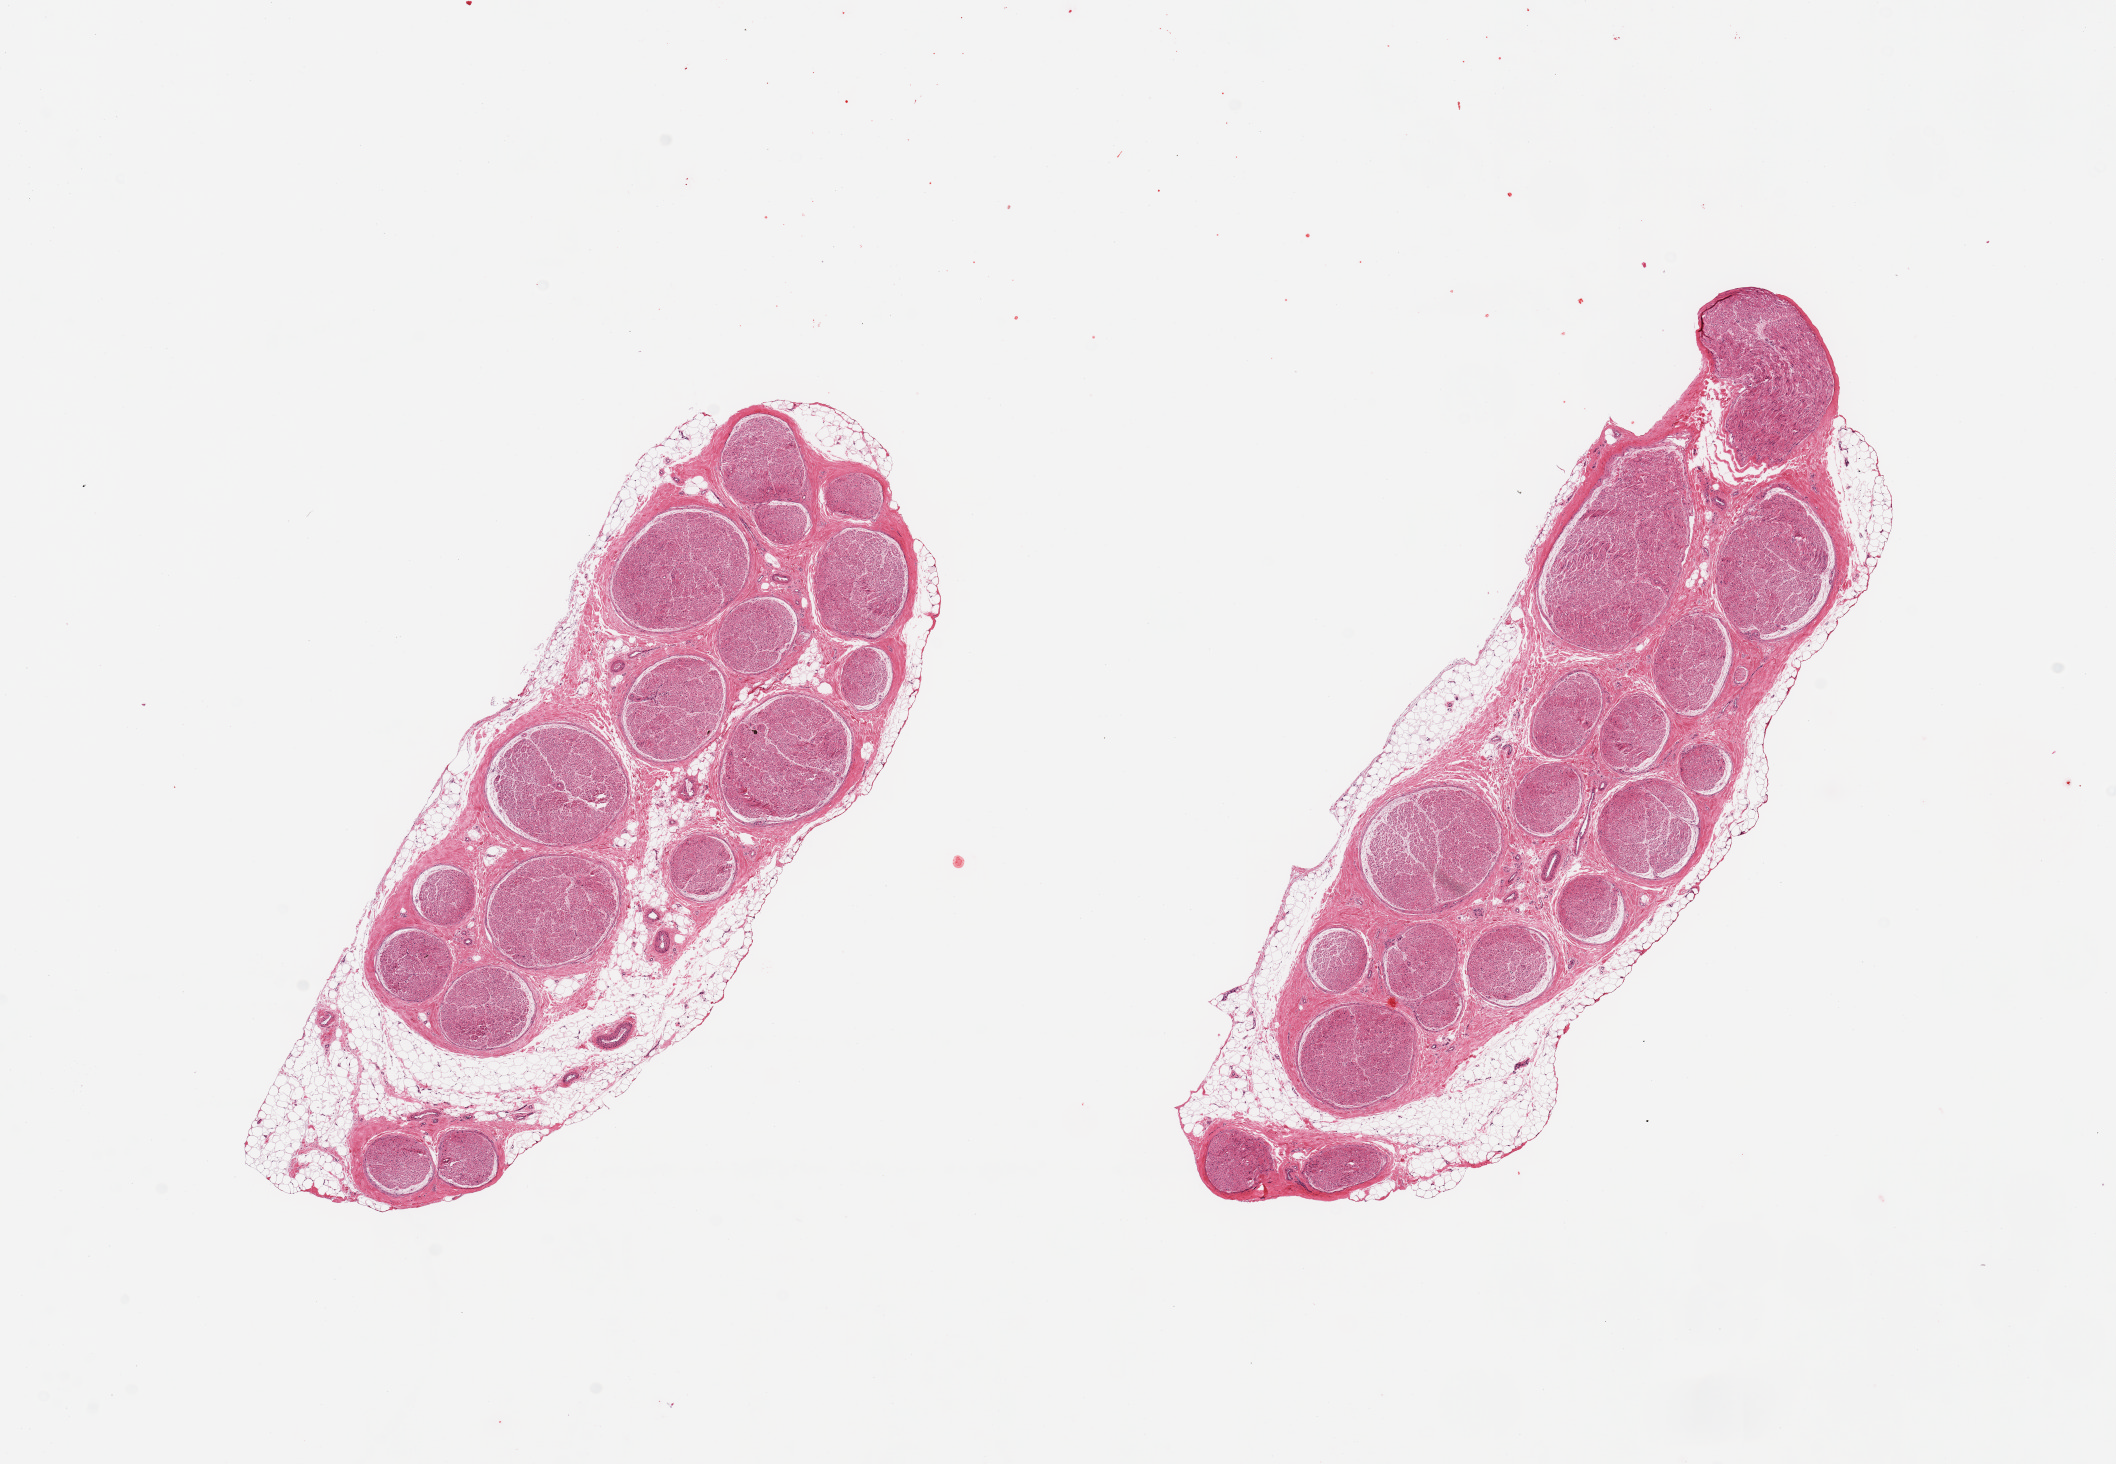
Digitized haematoxylin and eosin-stained section, a low-resolution overview of the entire scanned area, about 16.7 x 11.6 mm (slide scanned at 20x). PAXgene-fixed, paraffin-embedded tissue. Section of tibial nerve (target tissue). Tissue donor sample. Donor sex: male.
* review note (as recorded): 2 pieces; ~10% external rim of fat